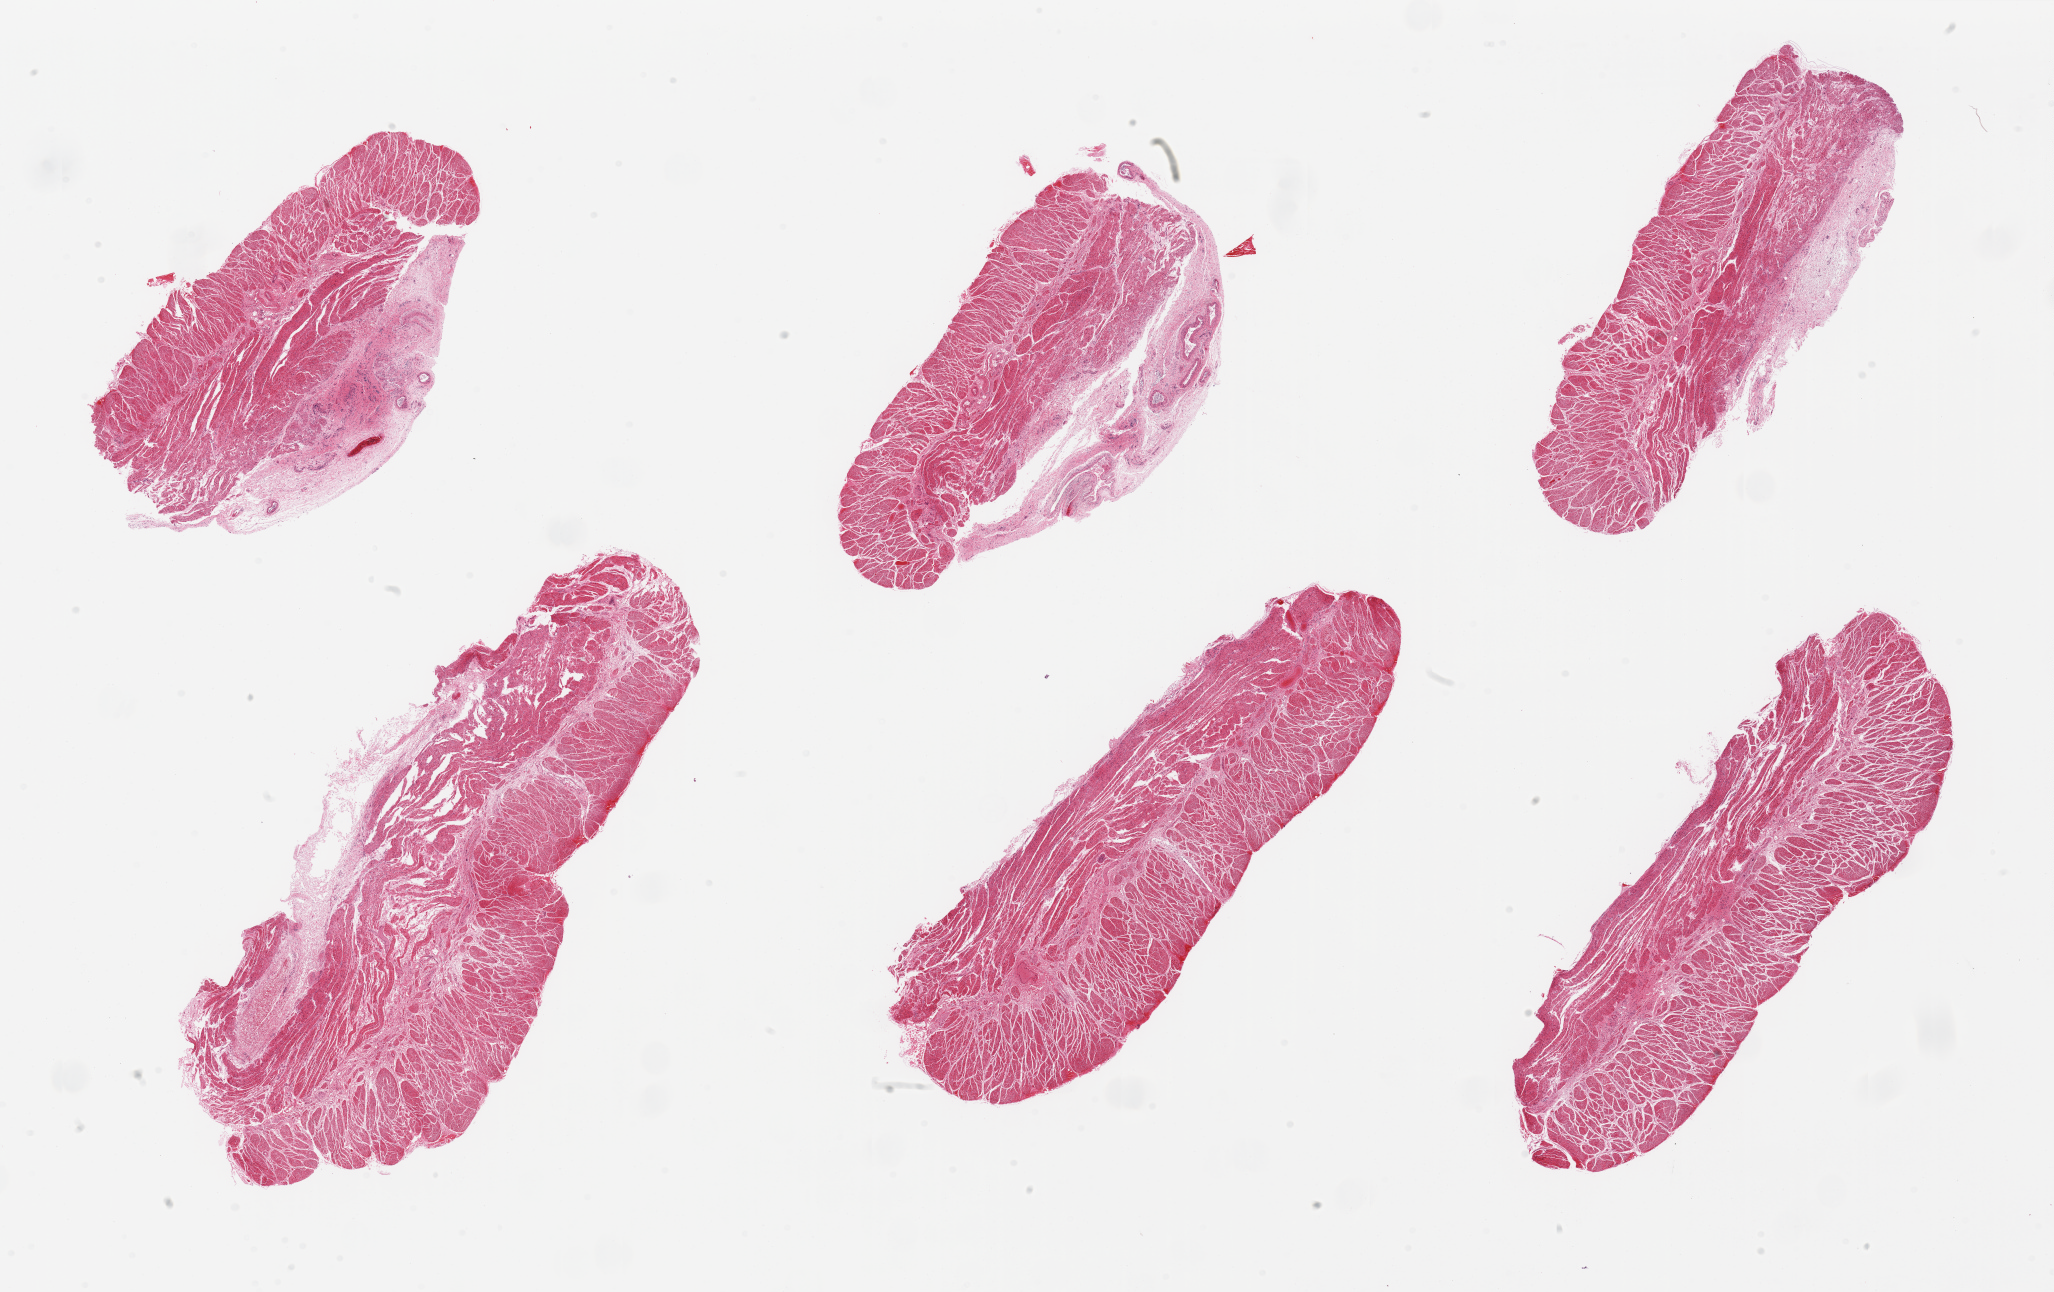
Digitized H&E-stained section, low-resolution overview of the scanned area, about 32.5 x 20.4 mm (acquisition: 20x scan). PAXgene-fixed, paraffin-embedded tissue. Target tissue: esophageal muscle. Tissue donor sample.
• review note (as recorded): 6 pieces, all muscularis